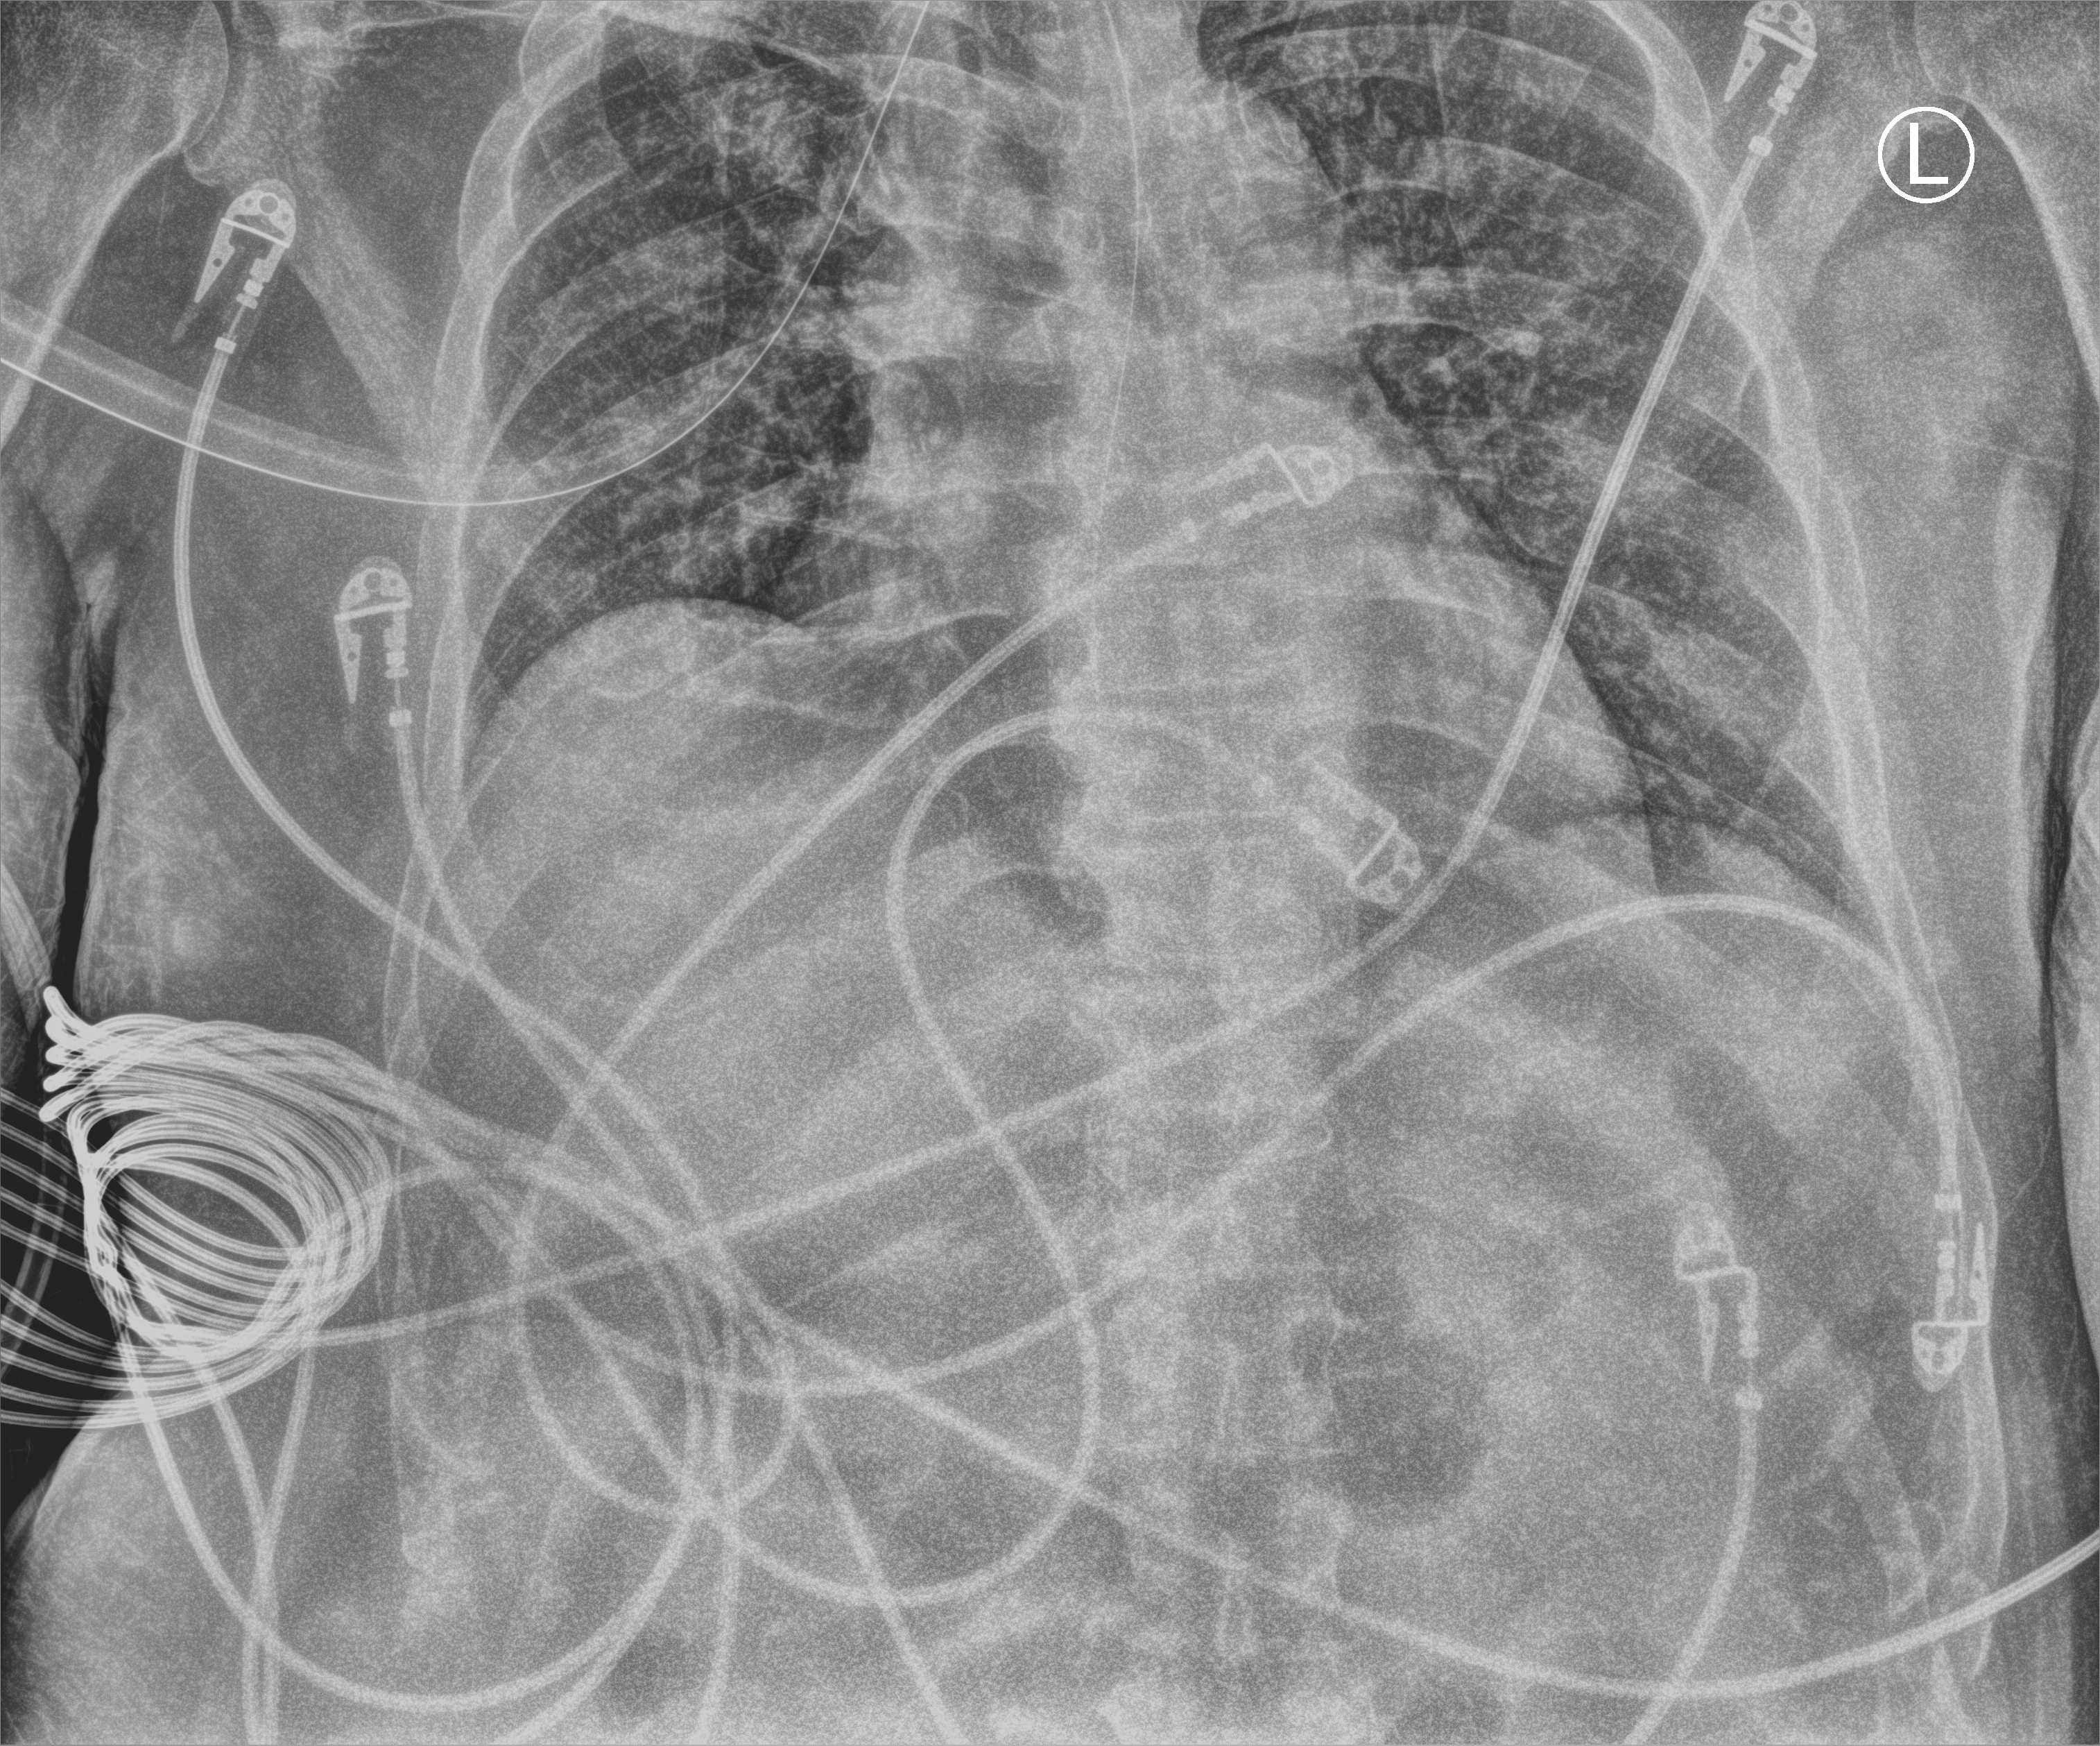
Portable chest radiograph, anteroposterior (AP) projection. Adult patient hospitalised with COVID-19, age 18–59 years.
From the hospital-stay record, not from the radiograph (when in the stay this image was taken is not recorded):
- COPD (admission record): no
- admitted to intensive care during this hospital stay: yes